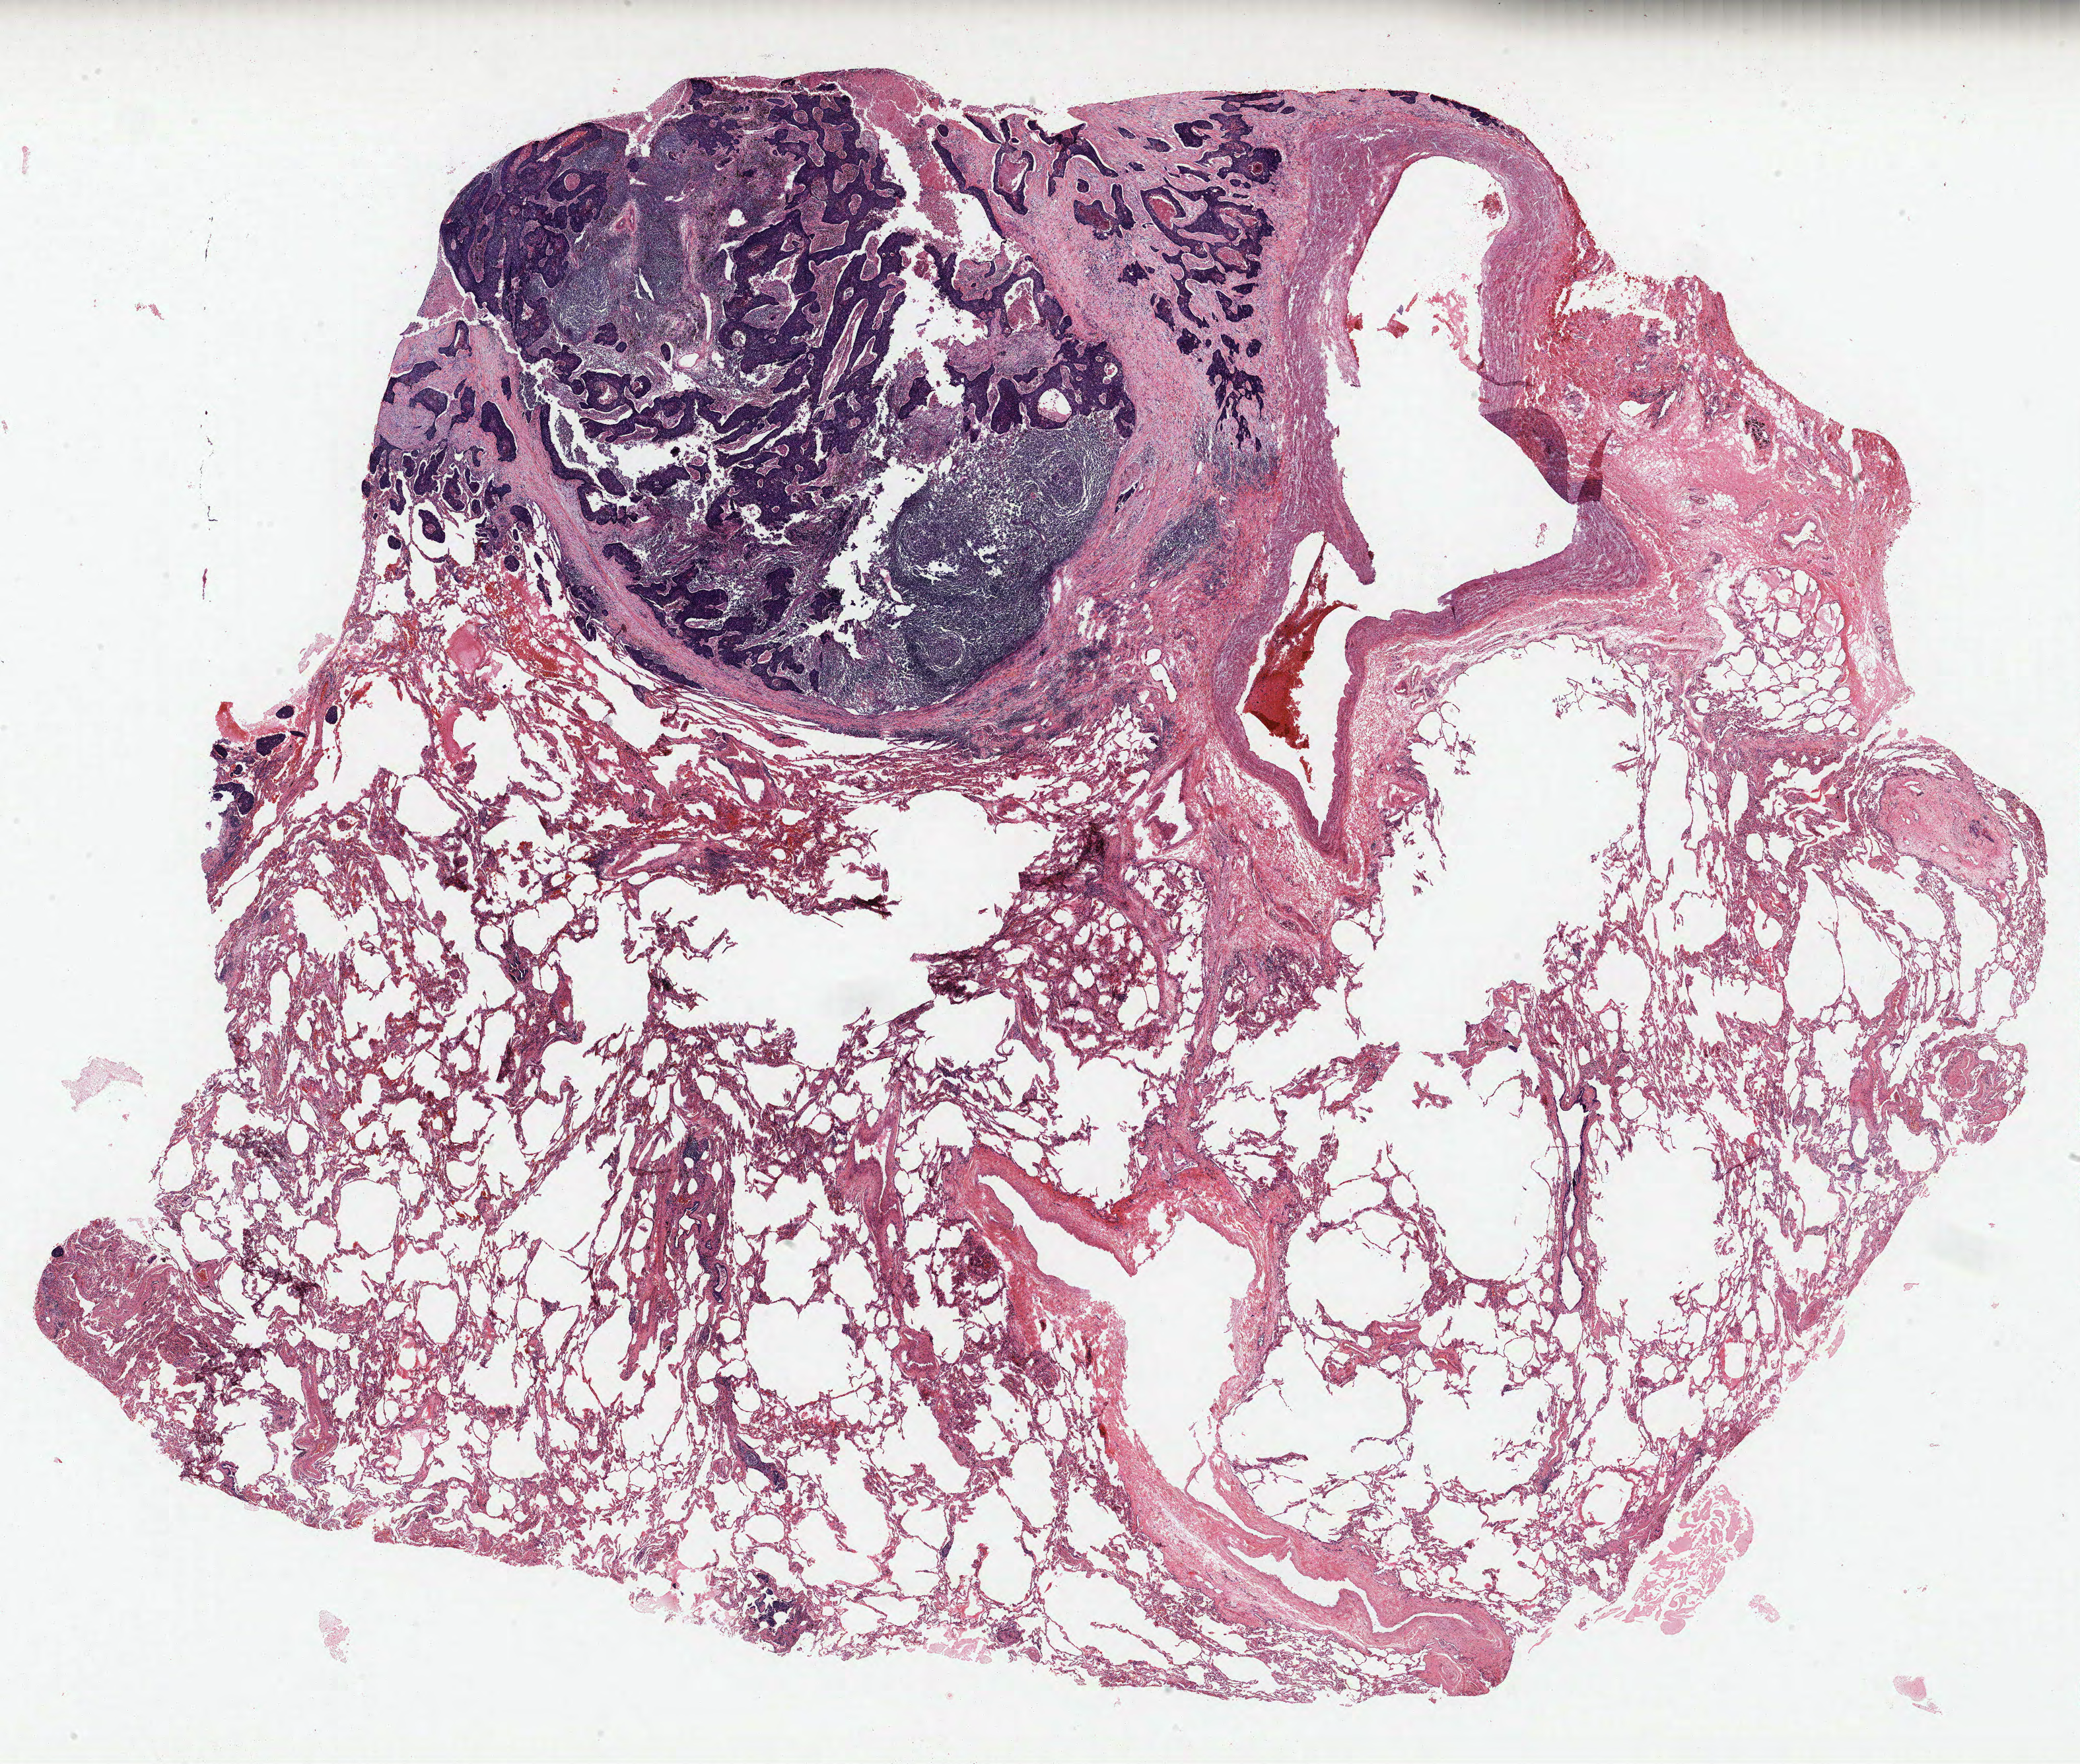
H&E whole-slide image, shown as a low-resolution overview of the whole scanned area (about 25.2 x 21.4 mm). FFPE section. Lung. Female, age 57 at enrolment. Current smoker at enrolment. Grade: moderately differentiated (G2).
Primary tumour location (clinical record): left lower lobe. Participant's lung-cancer diagnosis: Basaloid squamous cell carcinoma. Stage (AJCC 6th edition): IIB. ICD-O-3 topography: lower lobe of lung (C34.3). Tumour size (pathology): 32 mm.